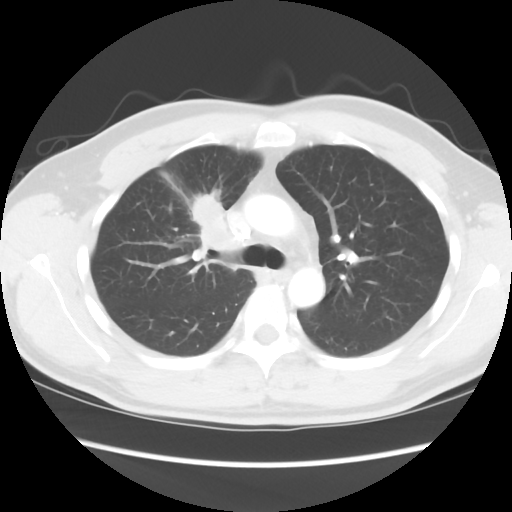
Chest CT, one axial slice. Slice 62 of 80 in the series (ordered by position). Reconstruction kernel STANDARD. 120 kVp. Lung window (W 1500 / L -600 HU). 5 mm slice thickness. 512 × 512 image matrix. Male patient, age 35 years. Case-level facts recorded for this patient, not image findings: clinical TNM (as recorded): T1c N1 M1b.
Structures marked on this image (rectangle marked by the reading radiologist):
- lung tumour (recorded histology: adenocarcinoma): bounding box (x1, y1, x2, y2) in pixels: (189, 186, 237, 252)